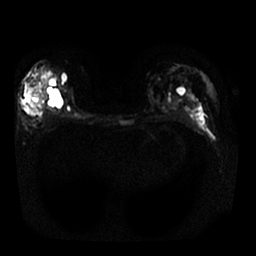
Breast MRI, one axial slice; position 16 of 30 along the scan axis; diffusion-weighted series; image 2 of 4 stored at this slice position (different b-values; order by instance number); 1.5 T; 4 mm slice thickness; 256 × 256 image matrix, field of view 340 × 340 mm. Female patient.
Annotated regions visible in this slice (expert manual segmentation):
- tumour on diffusion-weighted imaging: bounding box [x1, y1, x2, y2] px = [26, 97, 45, 113]